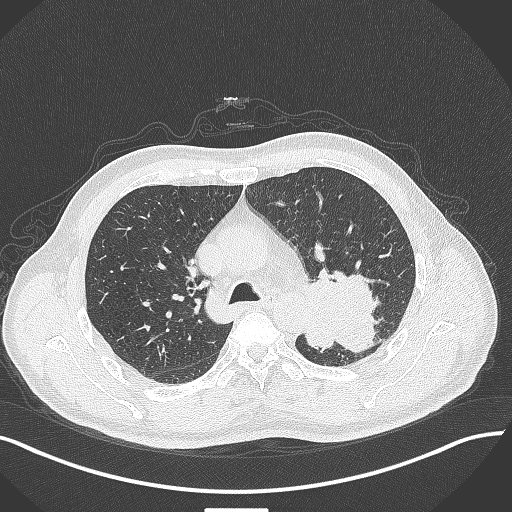
Chest CT, one axial slice. Slice 288 of 429 in the series (ordered by position). Reconstruction kernel B70f. Lung window (W 1500 / L -600 HU). 512 × 512 image matrix. Male patient, age 55 years. Case-level facts recorded for this patient, not image findings: clinical TNM (as recorded): T3 N0 M1c; histopathological grade: G3.
Annotated regions visible in this slice (bounding box drawn by a radiologist):
- lung tumour (recorded histology: adenocarcinoma): bounding box <305,262,387,356> (left, top, right, bottom; pixels)